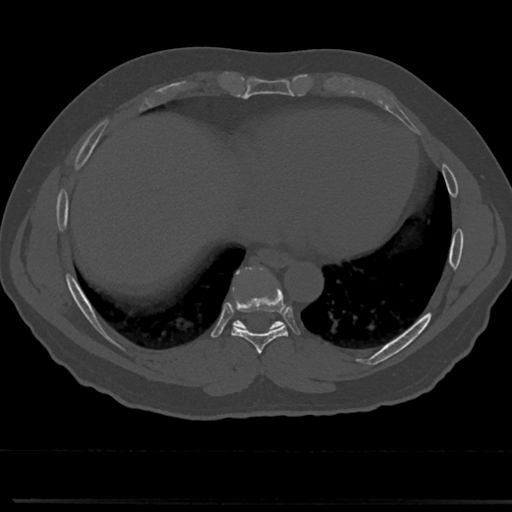
CT including the spine, one axial slice; position 341 of 817 along the scan axis; bone window (W 1800 / L 400 HU); 0.5 mm slice thickness; 512 × 512 image matrix, field of view 355 × 355 mm. Patient: male, 61 years. From the clinical record (not read from this slice): primary cancer: prostate.
Outlined on this slice (semi-automatic segmentation, software-assisted and operator-edited):
- T7 vertebra: bounding box [x1, y1, x2, y2] px = [257, 343, 268, 377]
- T8 vertebra: [214, 271, 308, 355]